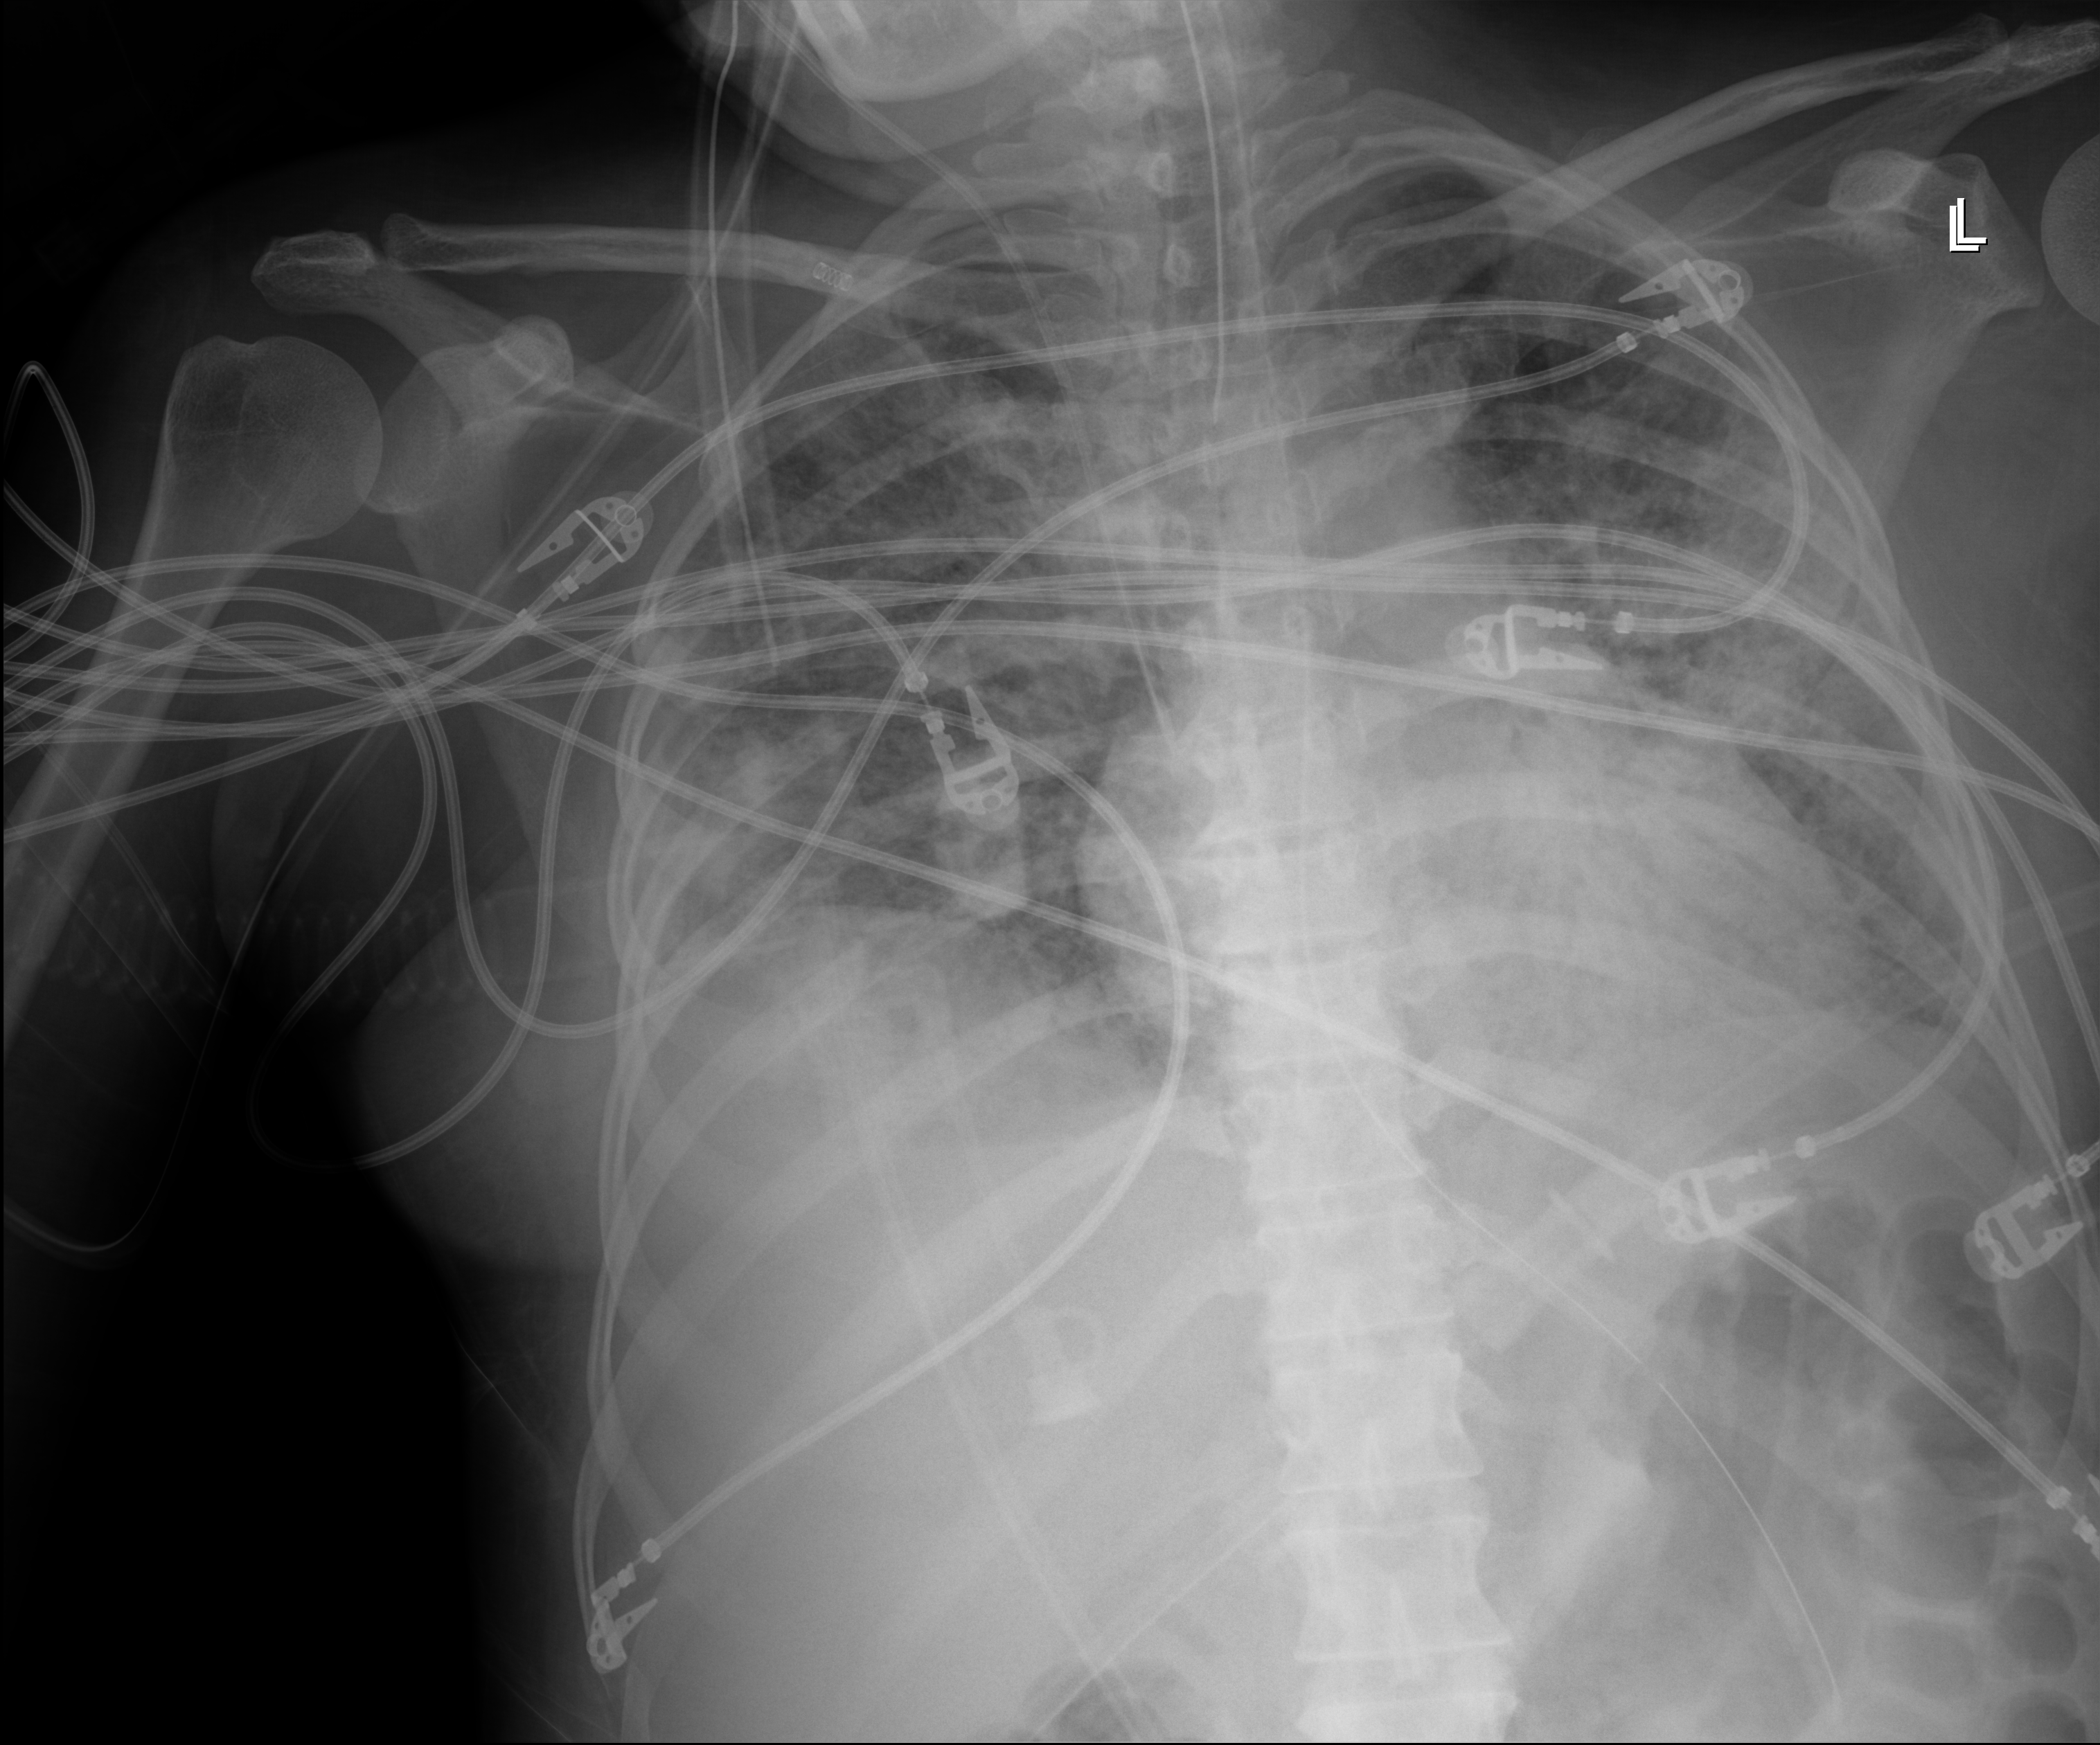
Portable chest radiograph; anteroposterior (AP) projection. Female patient hospitalised with COVID-19, age 18–59 years.
Admission-level facts for this patient (not findings on this image; timing relative to this image not recorded): length of hospital stay: 71 days; other chronic lung disease (admission record): no.